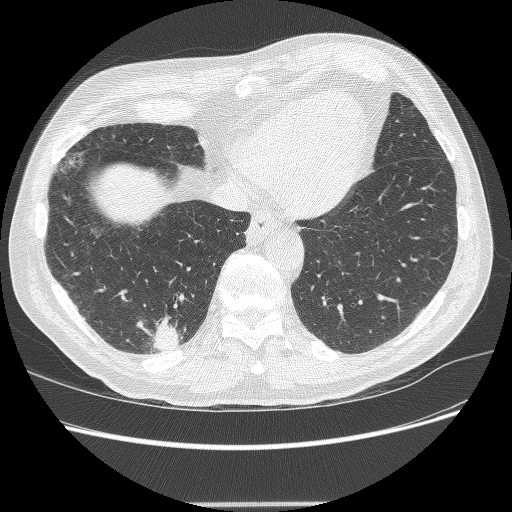
Low-dose screening chest CT, axial slice. Second screening round (one year after baseline). Lung window (W 1500 / L -600 HU). Male, age 71 years at enrolment.
Expert-annotated lung lesion, bounding box (x1, y1, x2, y2) in pixels: (137, 322, 187, 360). The screening reader recorded 5 non-calcified nodules or masses ≥4 mm on this exam (right lower lobe, right lower lobe, right upper lobe, right upper lobe, right upper lobe); which of them this box marks is not recorded.